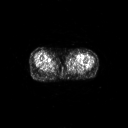
FDG PET of an extremity soft-tissue mass (from a PET/CT study), one axial slice. Position 56 of 91 along the scan axis. 3.27 mm slice thickness. 128 × 128 image matrix. Female patient, age 74 years. Case-level facts recorded for this patient, not image findings: histological type: pleomorphic leiomyosarcoma; grade: high; site of the primary tumour: left thigh.
Annotated regions visible in this slice (expert contour drawn on MRI and transferred to this co-registered scan by the dataset authors):
- gross tumour volume including surrounding oedema: bounding box (x1, y1, x2, y2) in pixels: (67, 54, 73, 59)